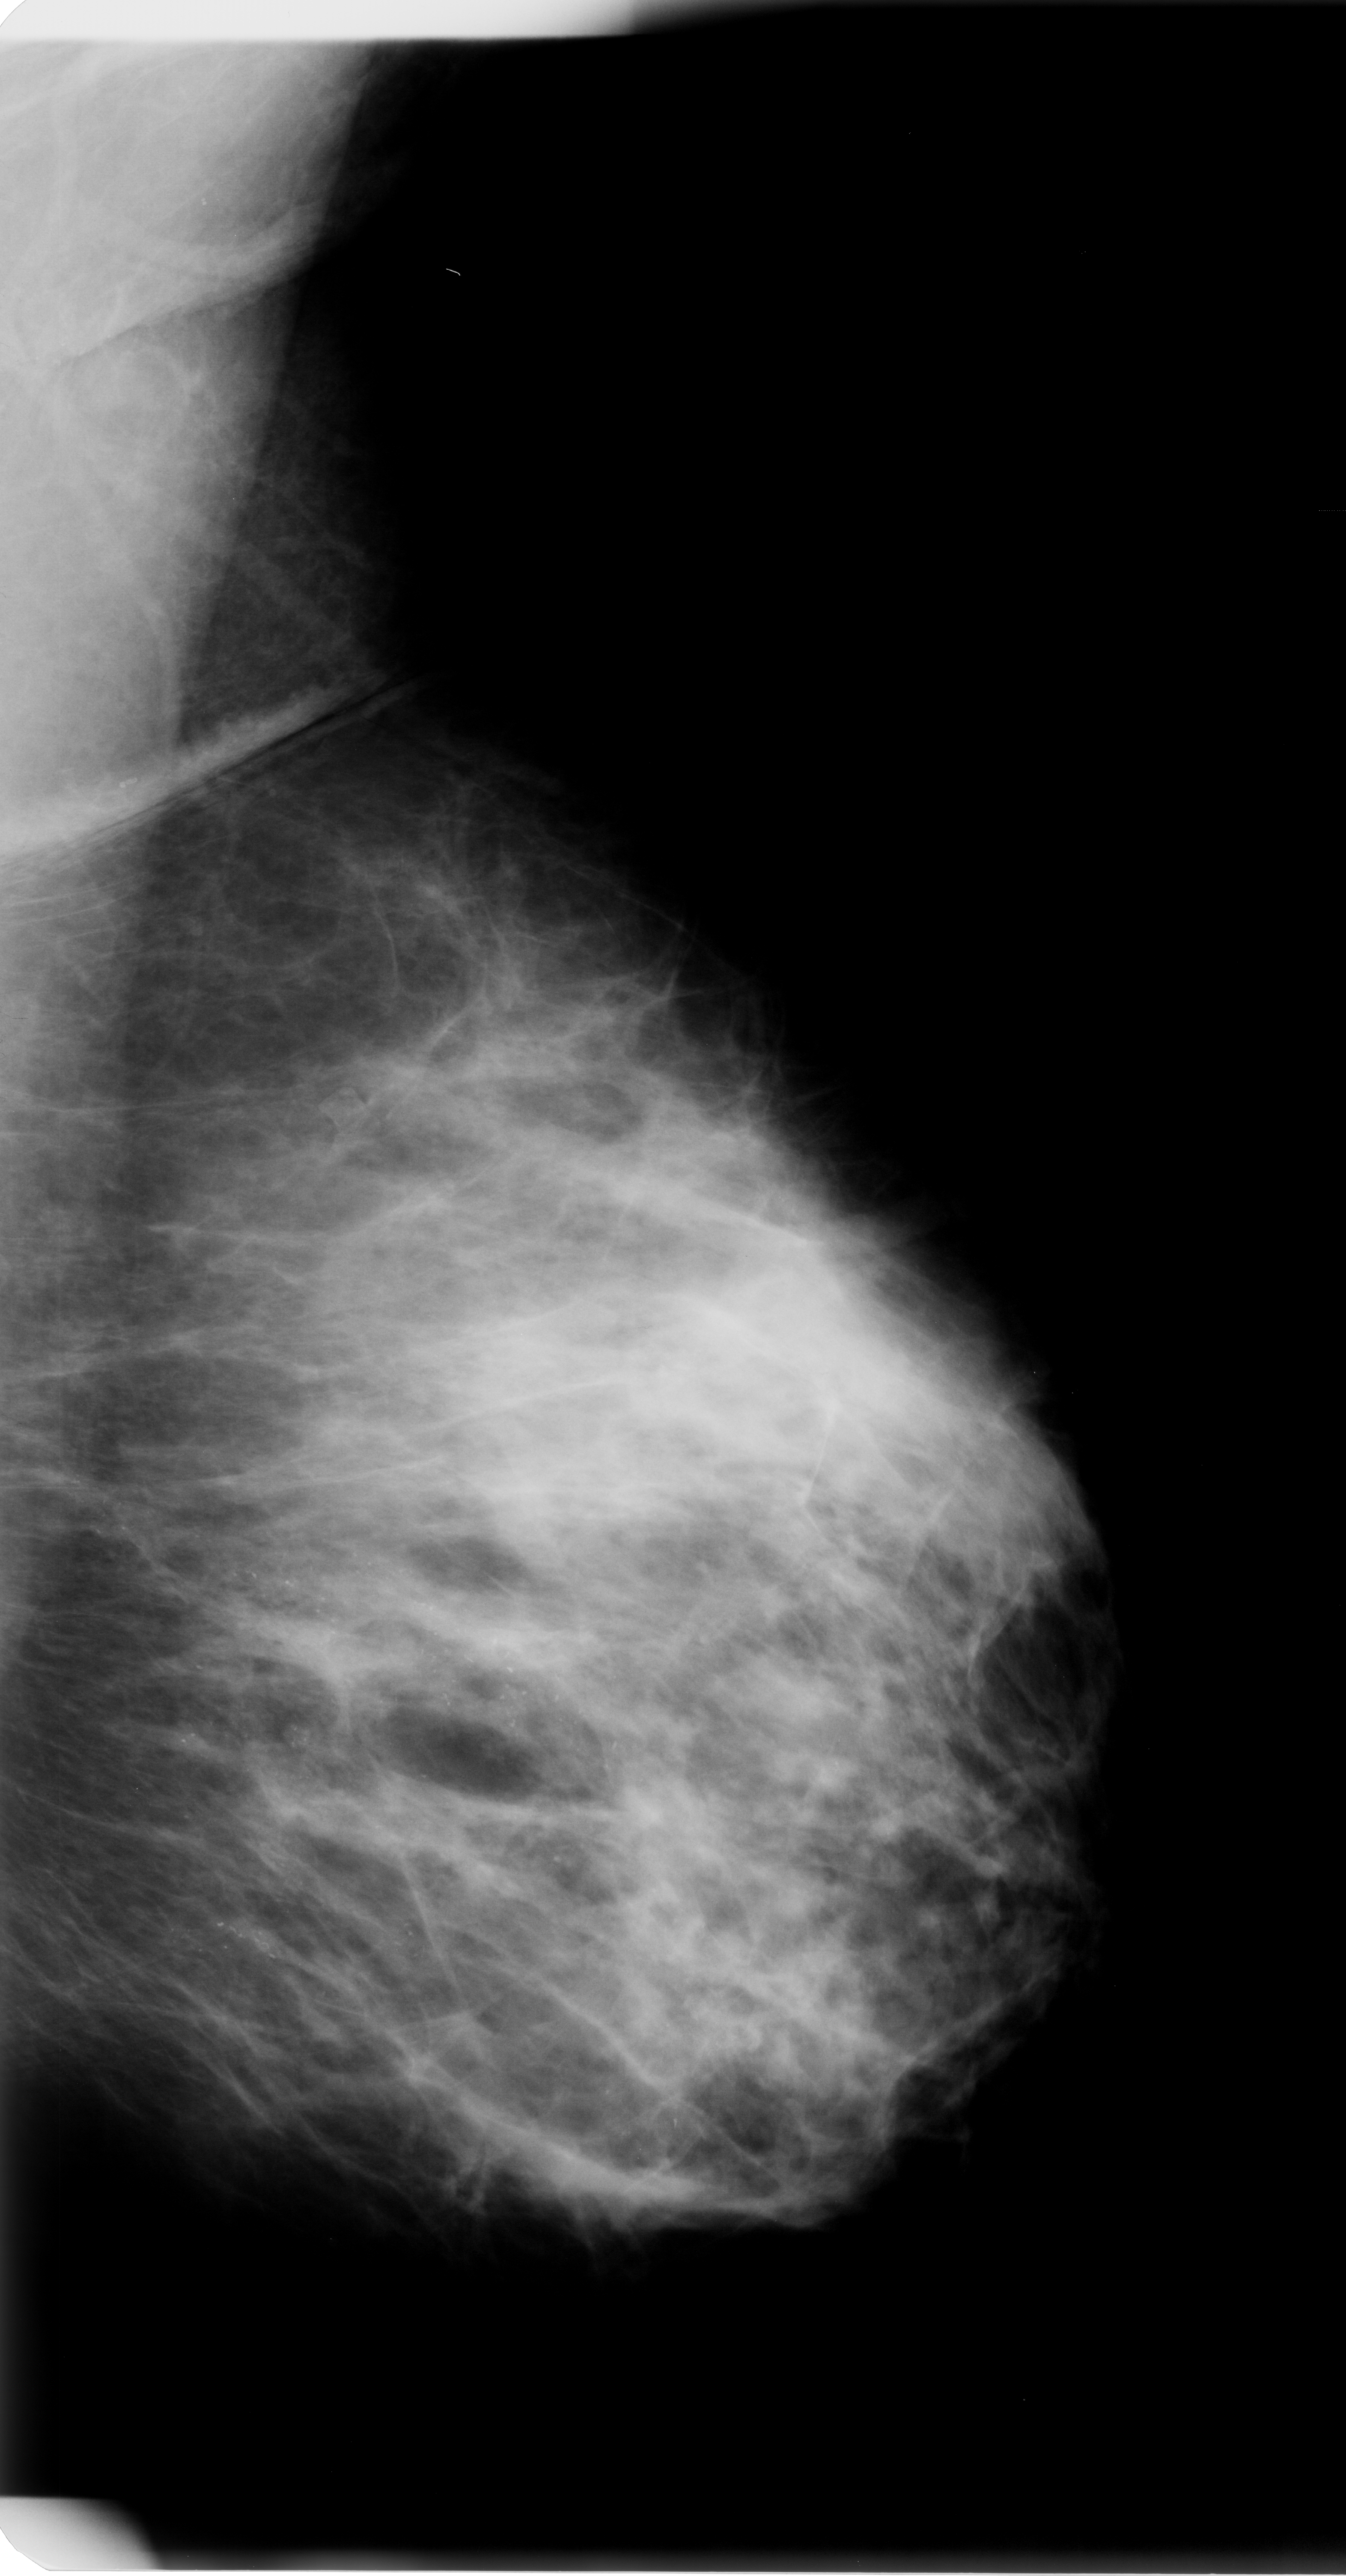
Digitized screen-film mammogram, left breast, mediolateral oblique (MLO) view, BI-RADS breast density category 2 (scale 1–4).
Marked findings (only marked abnormalities are described; nothing is implied about the rest of the image): calcifications, morphology pleomorphic, distribution regional; BI-RADS assessment category 5; subtlety rating 5 on a 1 (subtle) to 5 (obvious) scale; pathology result (as recorded, not read from the image): malignant.